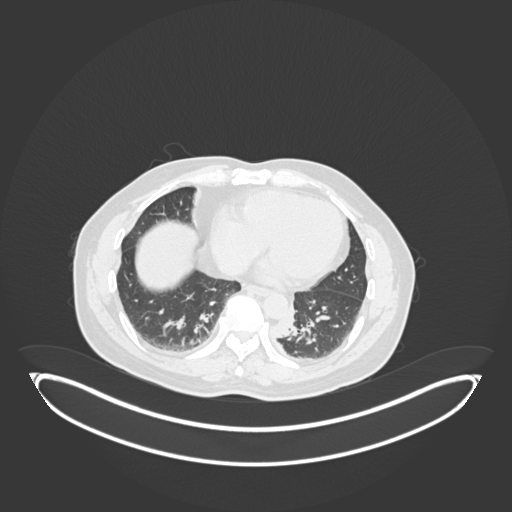
Chest CT, one axial slice; position 53 of 258 along the scan axis; reconstruction kernel B30f; 120 kVp; lung window (W 1500 / L -600 HU); 512 × 512 image matrix. Male patient, age 54 years. From the clinical record (not read from this slice): clinical TNM (as recorded): T3 N0 M0.
Structures marked on this image (rectangle marked by the reading radiologist):
- lung tumour (recorded histology: squamous cell carcinoma): box from (x=278, y=304) to (x=298, y=344) px